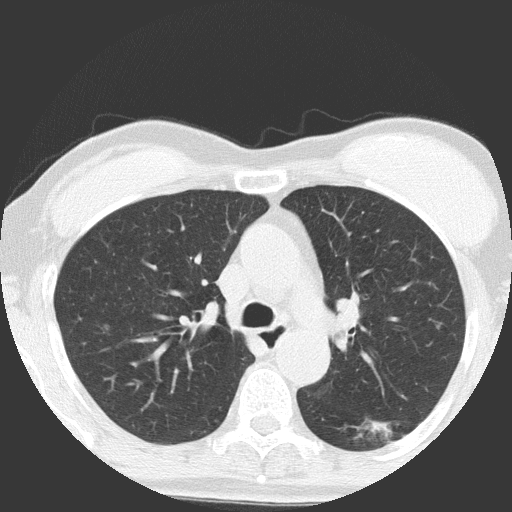
Chest CT (low-dose screening protocol), one axial image; baseline annual screen; lung window (W 1500 / L -600 HU); 2 mm slice thickness. Female, age 64 years at enrolment. Former smoker at enrolment.
- Lesion marked by an expert reader, bounding box <331,399,420,469> (left, top, right, bottom; pixels).
- Reader record for this screening exam (exam-level; its link to the box is not recorded): non-calcified nodule or mass ≥4 mm, right upper lobe, 4 × 4 mm, poorly defined margins, ground glass attenuation.
- Note: the box lies in the patient's left hemithorax on this image, whereas the reader's record names the right lung; they may be different findings.
- Official screen result: positive, change unspecified: nodule(s) >= 4 mm or enlarging nodule(s), mass(es), or other non-specific abnormalities suspicious for lung cancer.
- Later outcome: lung cancer diagnosed 932 days after this screen (after the third annual screen) — adenocarcinoma, NOS, left lower lobe, moderately differentiated (G2), stage IA (AJCC 6th edition), 17 mm at pathology.